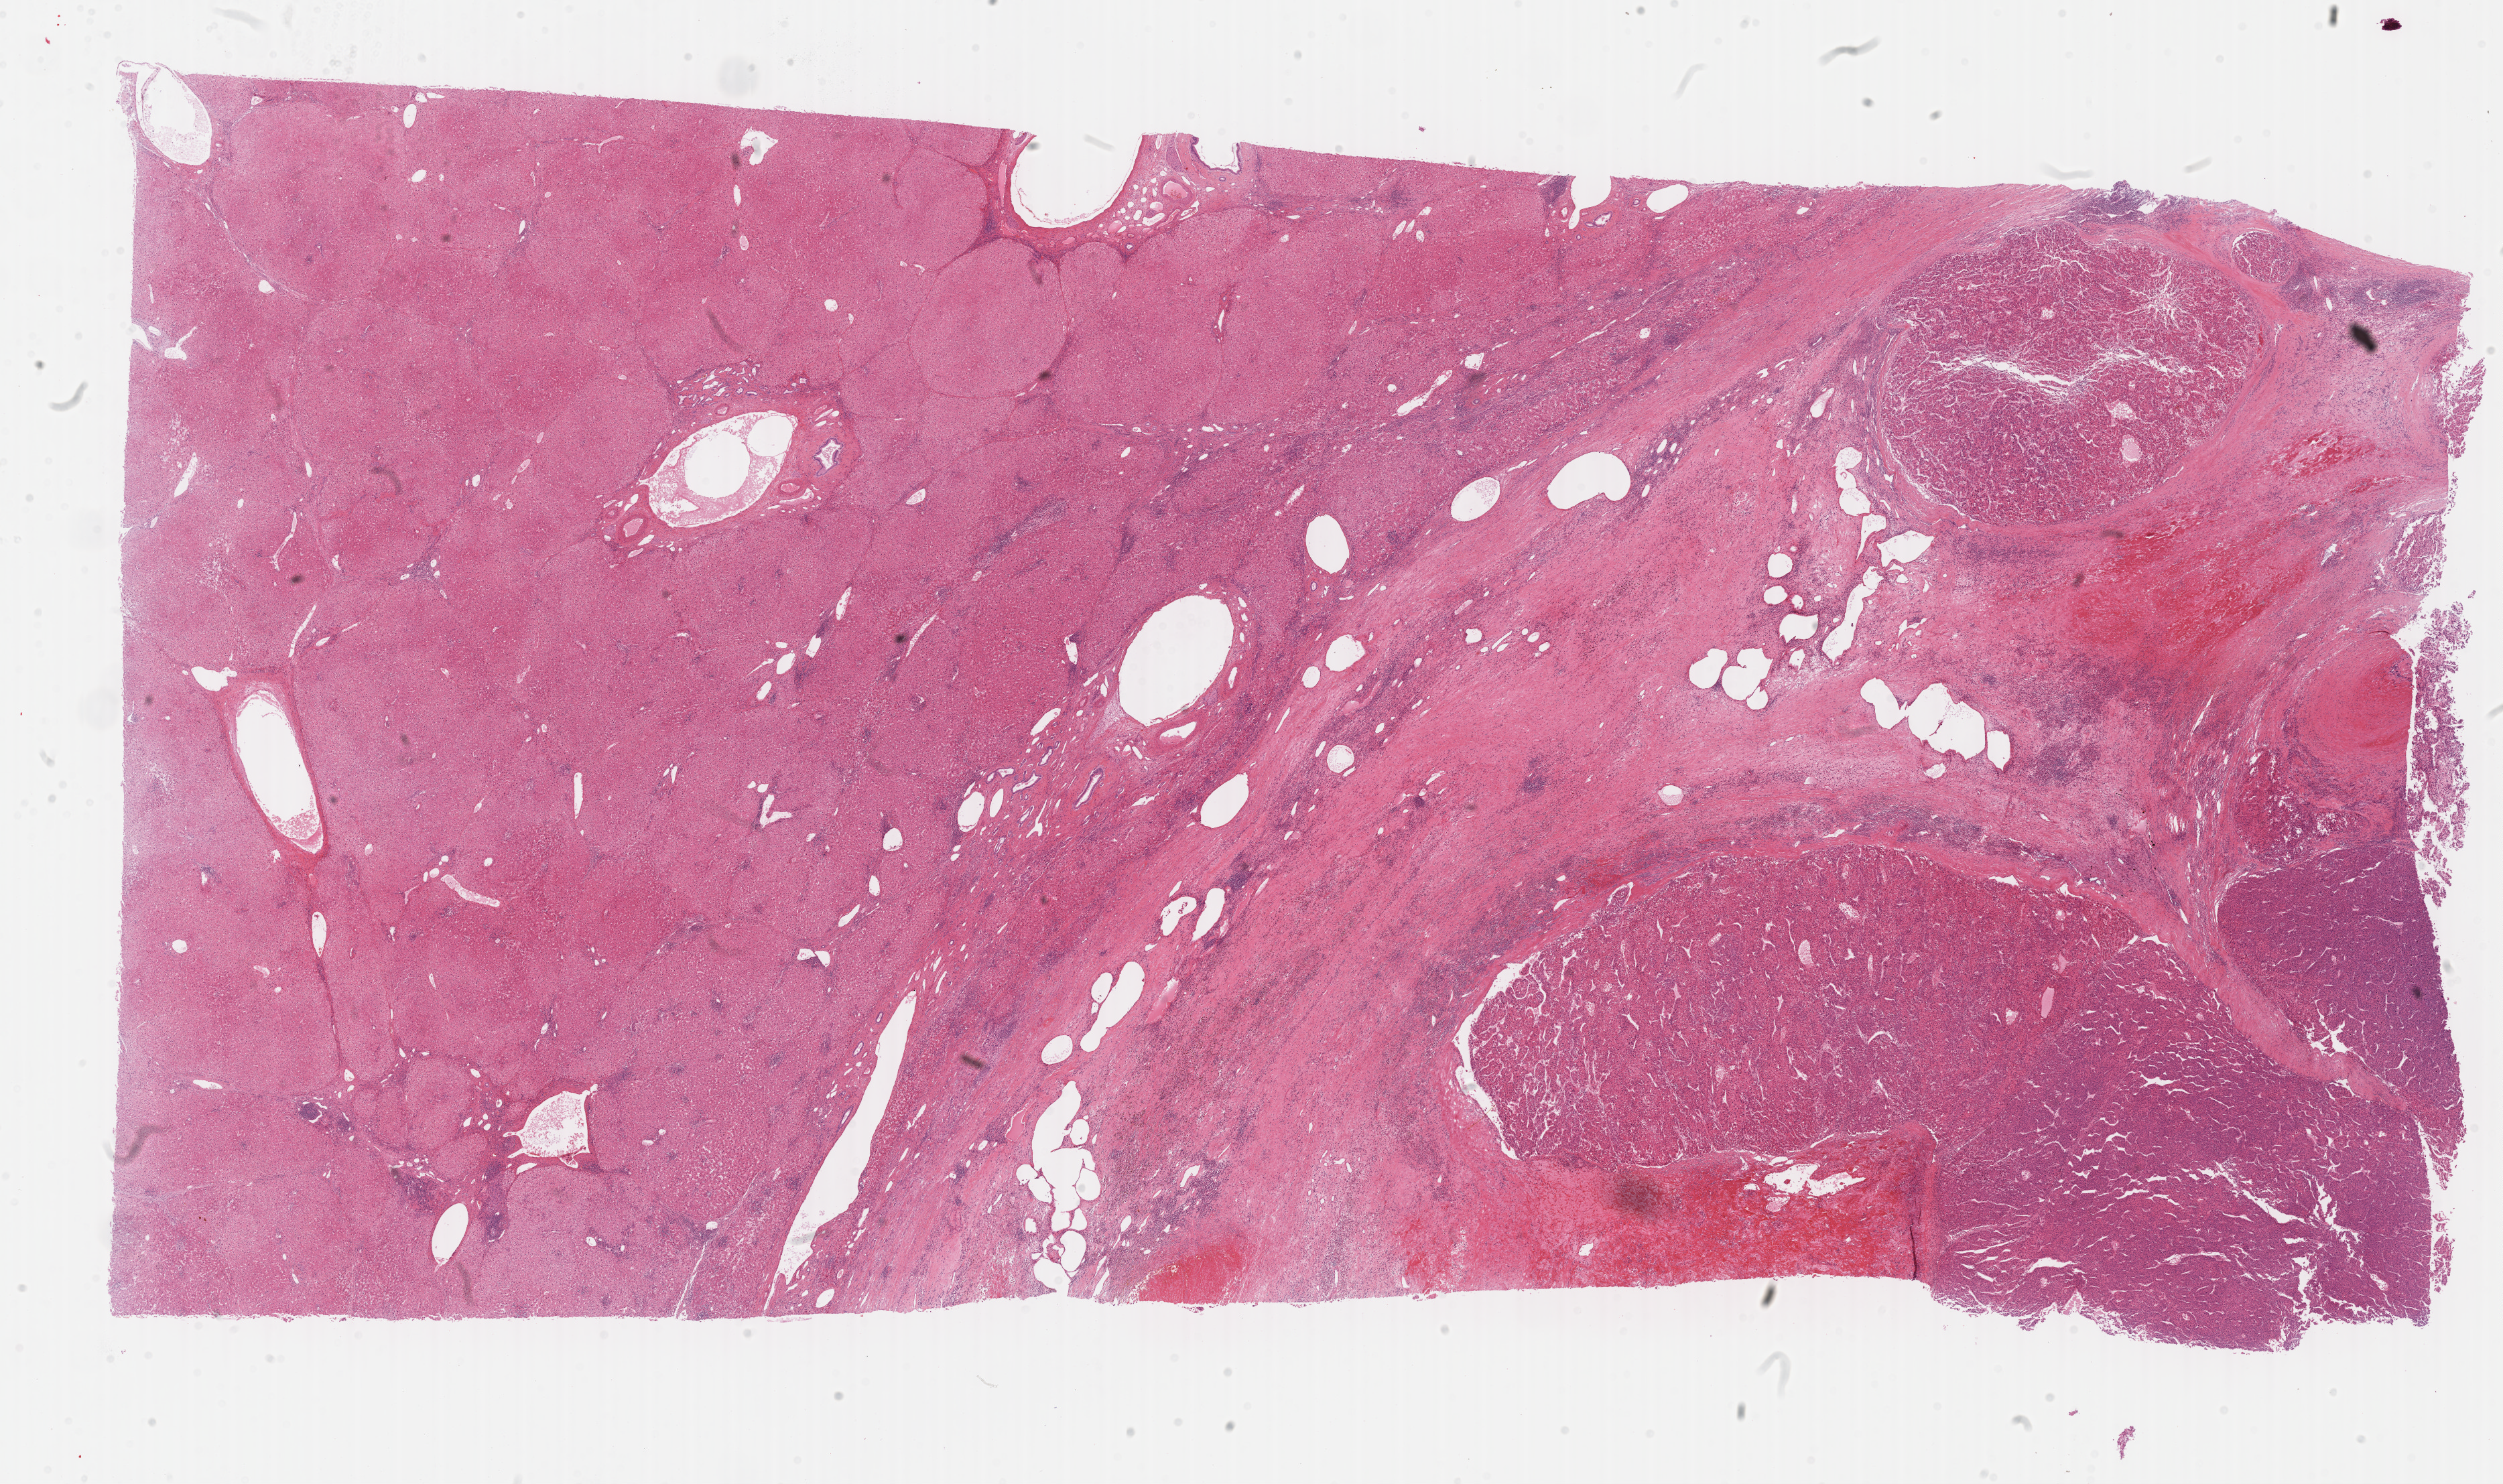
Whole-slide histology image, Hematoxylin and eosin (H&E) stained — low-resolution overview of the scanned area, about 30.2 x 17.9 mm (slide scanned at 40x); formalin-fixed paraffin-embedded (FFPE) diagnostic section; primary tumour sample from the liver. Patient: female, age at initial diagnosis 74 years.
Pathologic diagnosis: Hepatocellular carcinoma, NOS.